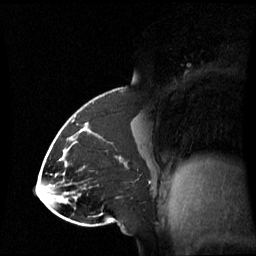
Breast MRI (dynamic contrast-enhanced), one sagittal slice; position 32 of 60 along the scan axis; dynamic contrast-enhanced series, image 2 of 3 at this slice position (ordered by acquisition); 1.5 T; TE 4.2 ms, TR 8.4 ms; 256 × 256 image matrix, field of view 270 × 270 mm. Female patient, age 43 years. Case-level facts recorded for this patient, not image findings: setting: breast cancer imaged before/during neoadjuvant chemotherapy; receptor status: triple-negative.
Outlined on this slice (semi-automatic segmentation, software-assisted and operator-edited):
- analysis volume of interest (the breast-tissue region the enhancement analysis was run in; not a lesion): bounding box (x1, y1, x2, y2) in pixels: (65, 118, 143, 198)
- tumour enhancement mask (voxels above the 70 % enhancement threshold inside the analysis volume of interest): (74, 142, 122, 161)